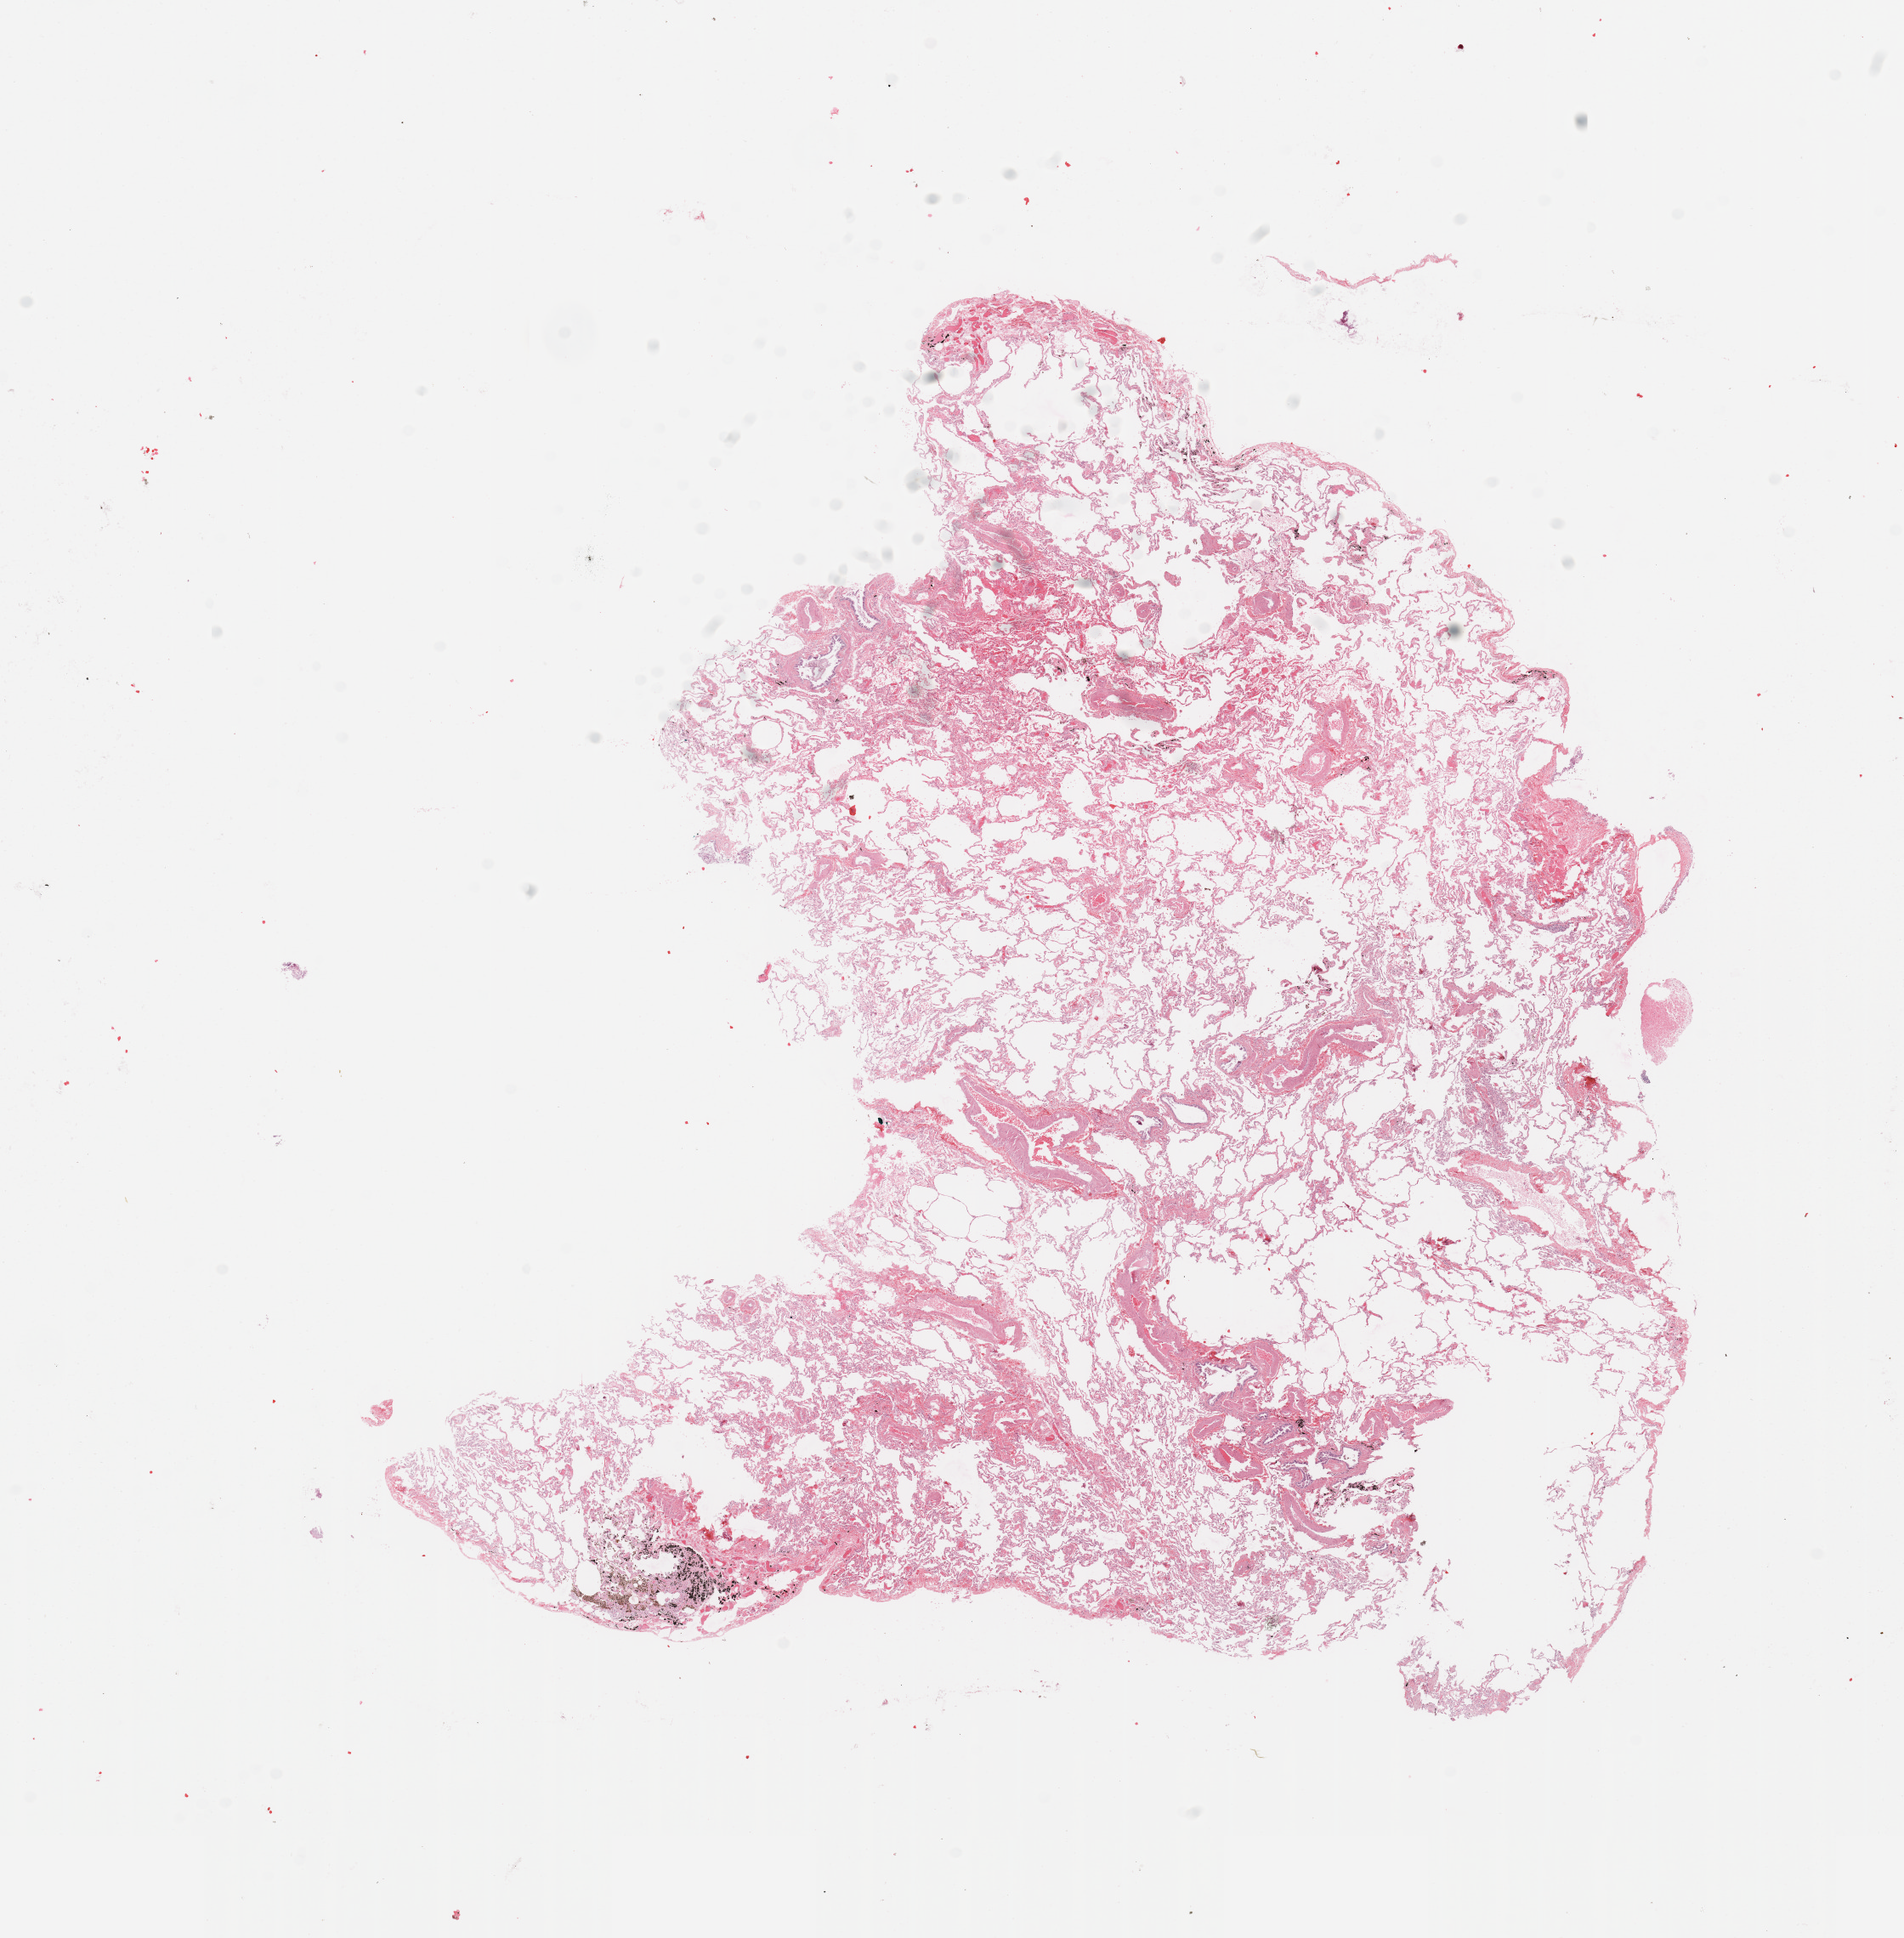
Whole-slide histology image, H&E-stained, whole scanned area (about 17.7 x 18.0 mm, acquisition: 20x scan) shown as a low-resolution overview. Normal (non-tumour) tissue sample, sampled site: lung. Patient: male, age 68 years.
This section: normal (non-tumour) tissue from the same patient. Patient diagnosis: Squamous cell carcinoma, NOS.